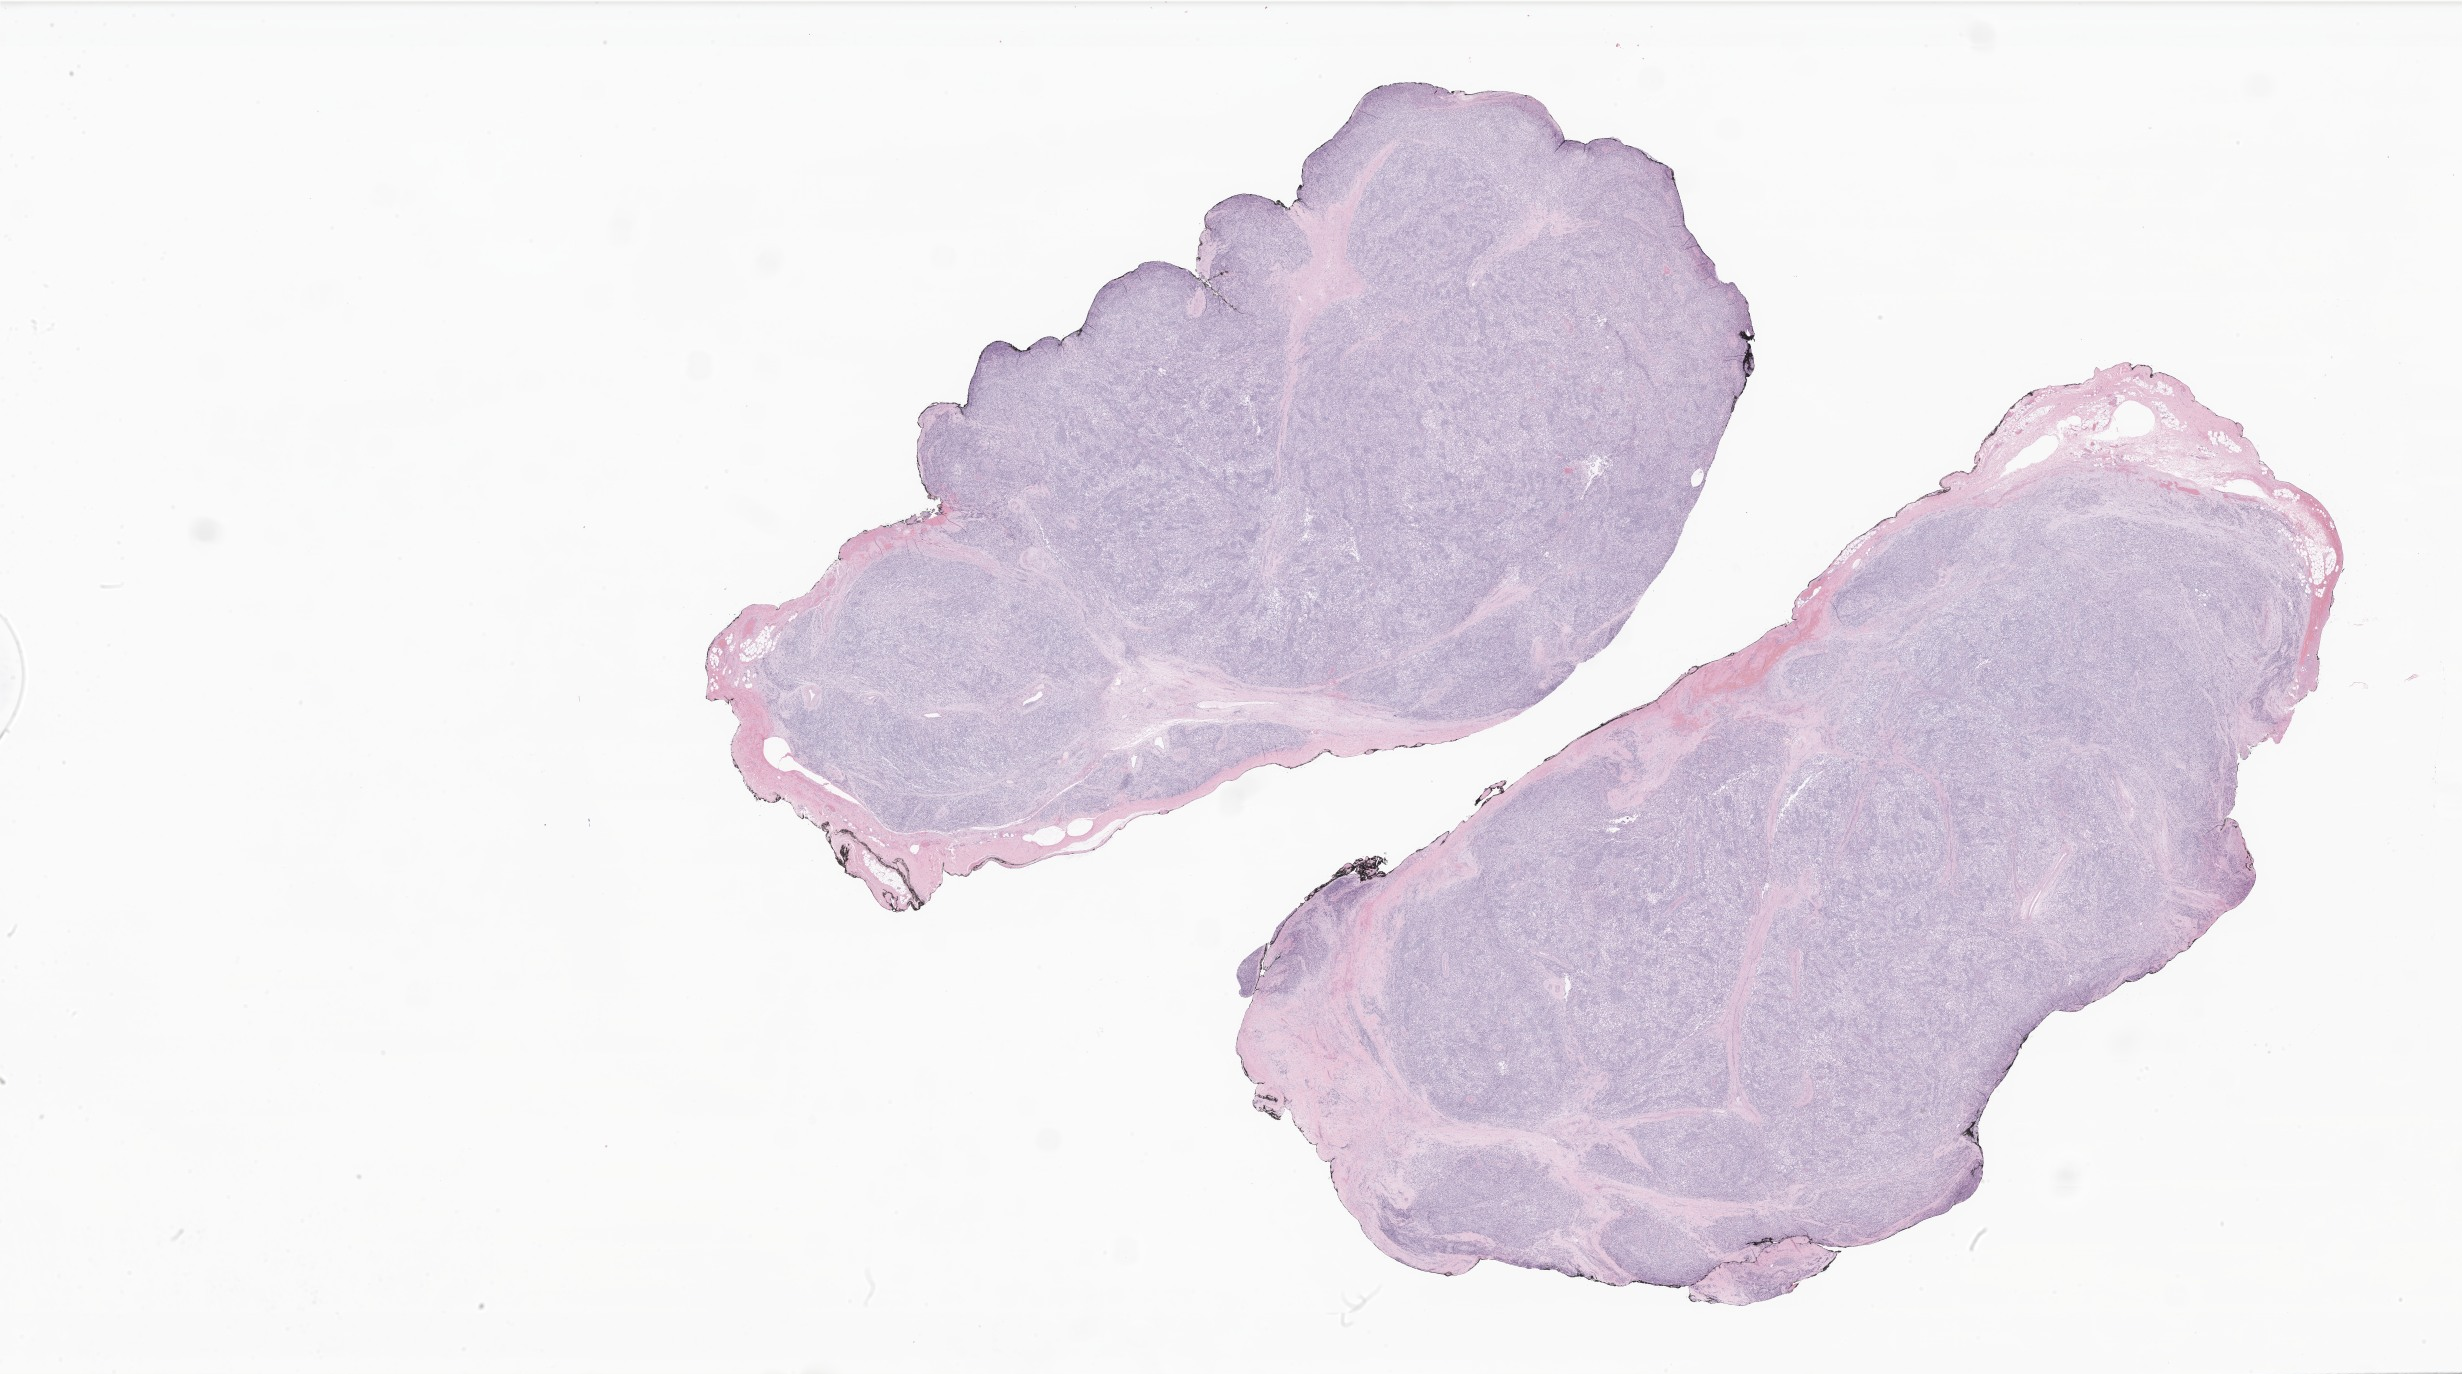
Whole-slide image, H&E stain of tumor tissue from the orbit — low-resolution overview of the scanned area, about 41.5 x 23.2 mm, FFPE section. Patient female; age 111 months (9 years 3 months).
Diagnosis: Embryonal rhabdomyosarcoma, NOS.